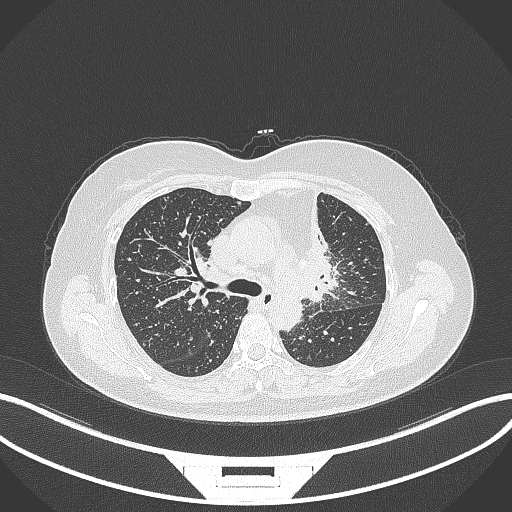
Chest CT, one axial slice. Slice 221 of 348 in the series (ordered by position). 120 kVp. Lung window (W 1500 / L -600 HU). 1 mm slice thickness. 512 × 512 image matrix, field of view 400 × 400 mm. Female patient, age 49 years. Case-level facts recorded for this patient, not image findings: clinical TNM (as recorded): T1c N0 M1.
Annotated regions visible in this slice (bounding box drawn by a radiologist):
- lung tumour (recorded histology: adenocarcinoma): bounding box (x1, y1, x2, y2) in pixels: (290, 189, 340, 303)